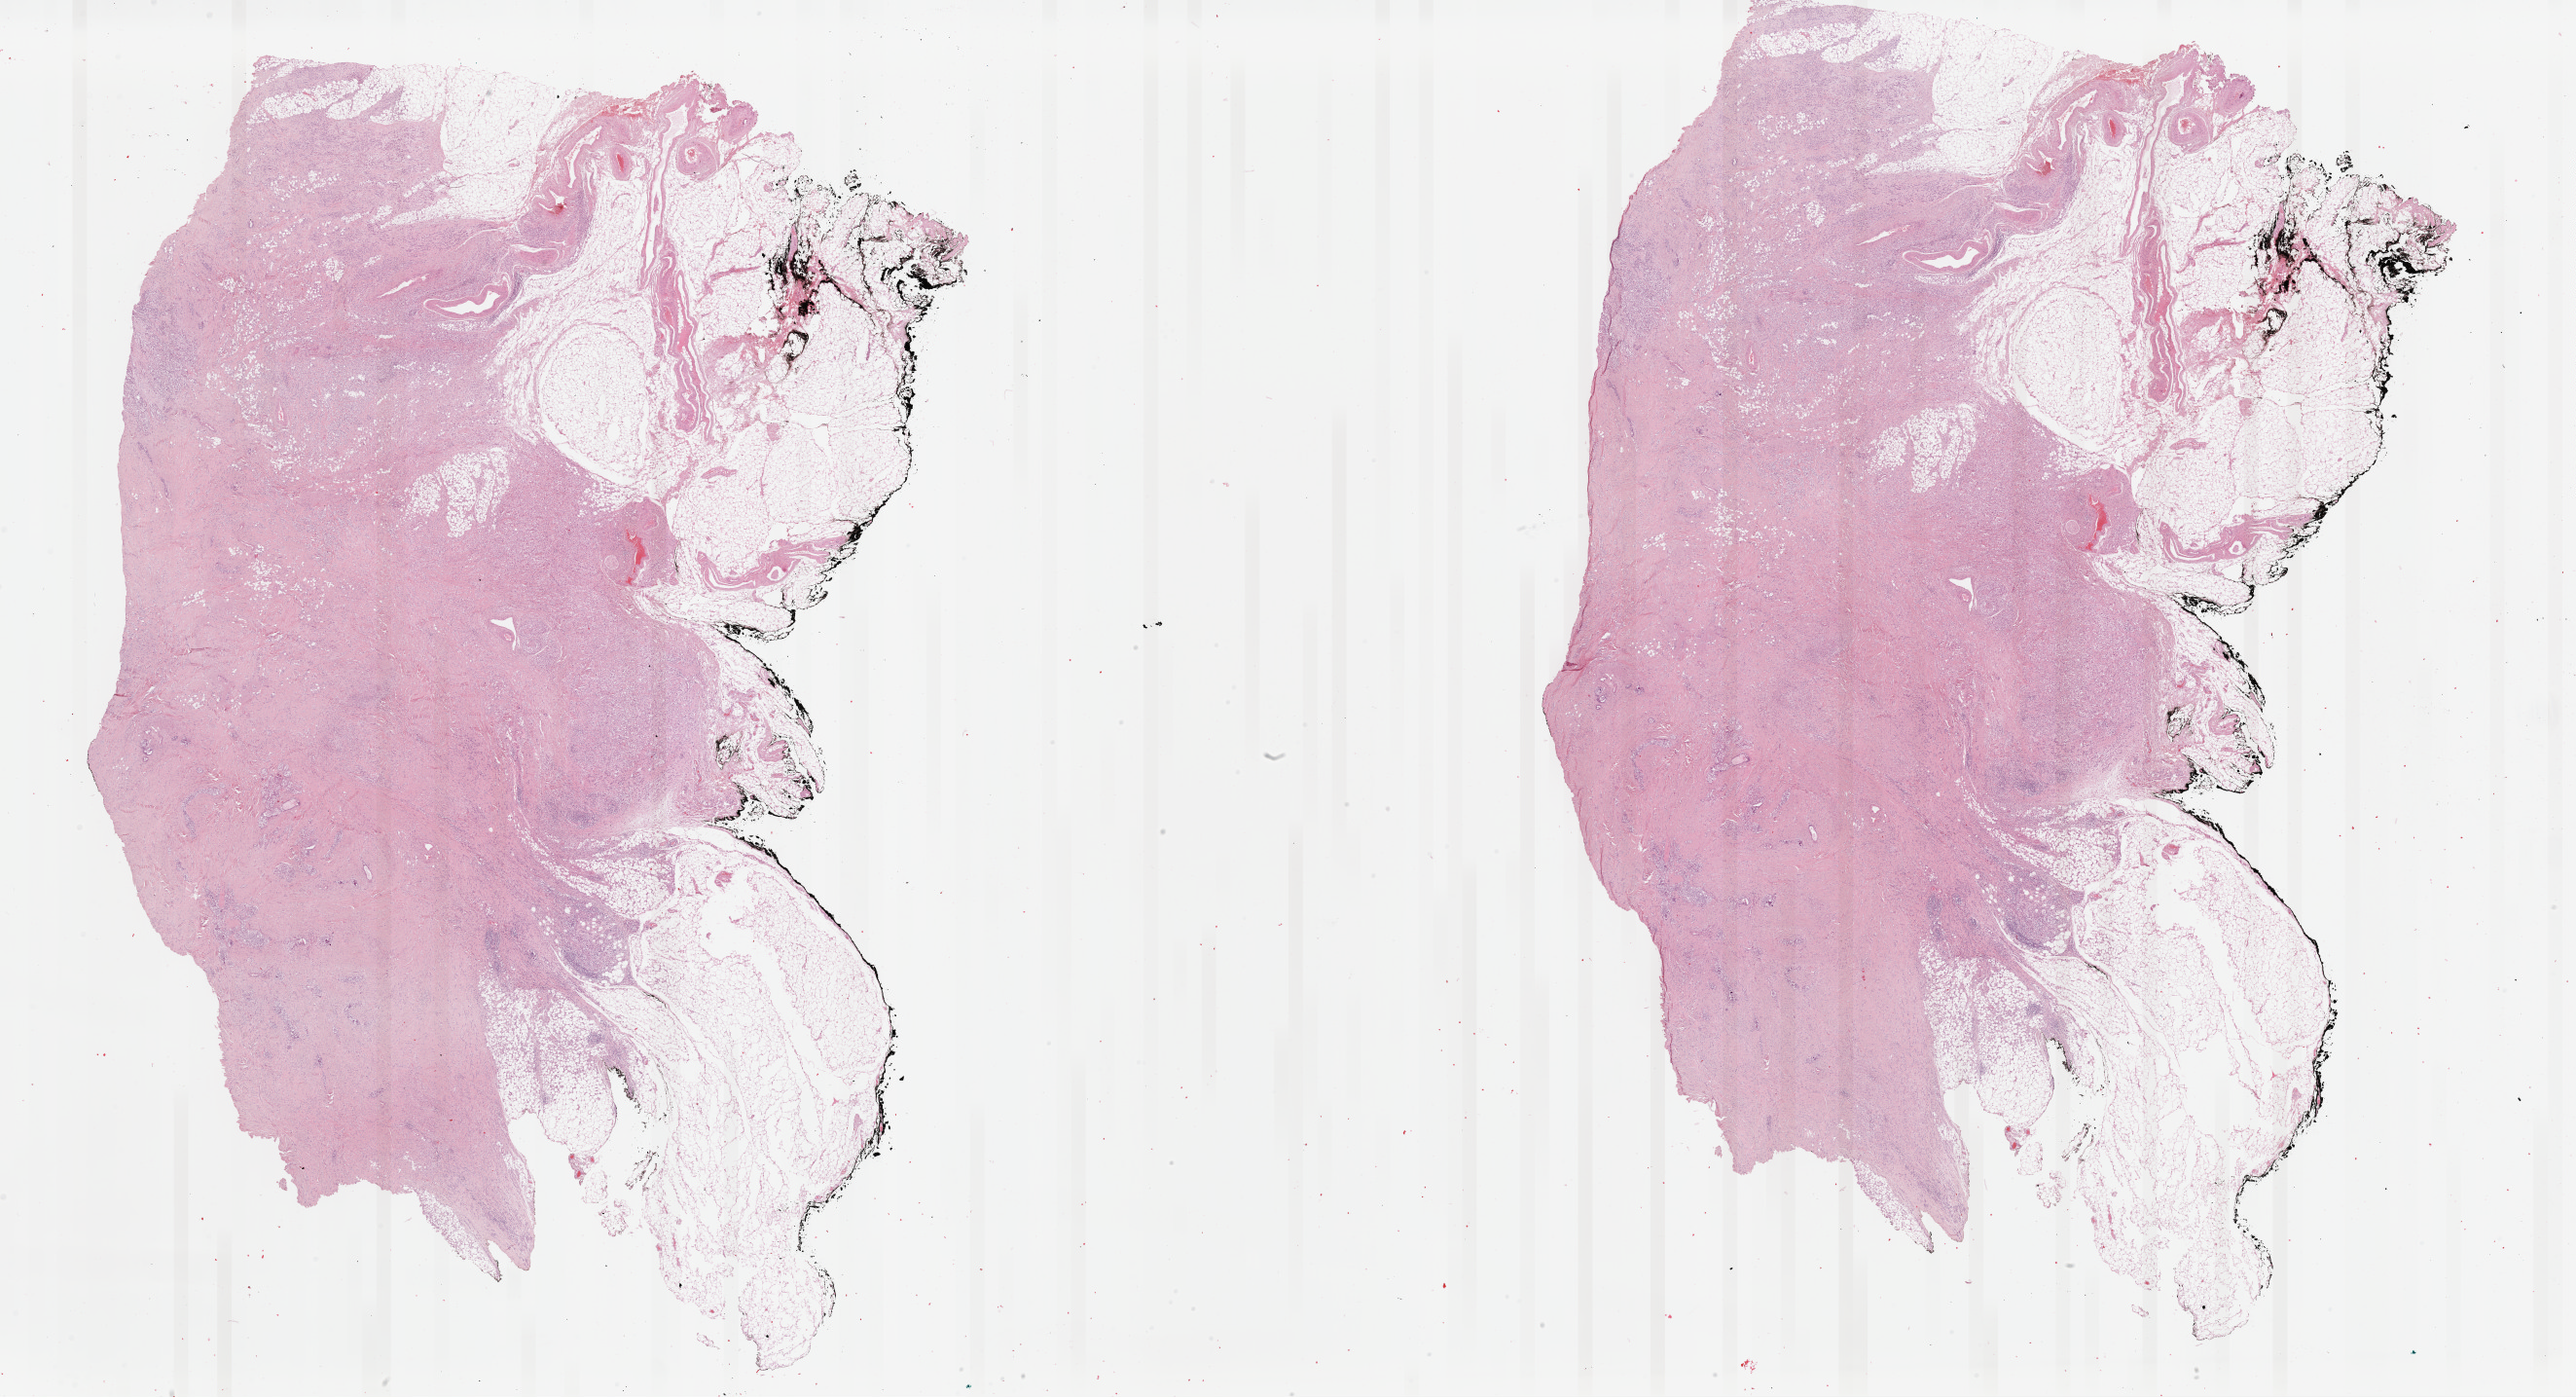
Digitized H&E tissue section (whole slide), a low-resolution overview of the entire scanned area, about 41.8 x 22.7 mm, FFPE section, primary tumour sample from the breast. Female, age 62 years at initial diagnosis.
* histologic diagnosis: Lobular carcinoma, NOS
* lymph nodes positive (case pathology): 0 of 2 examined
* AJCC pathologic stage: IIA (7th edition)